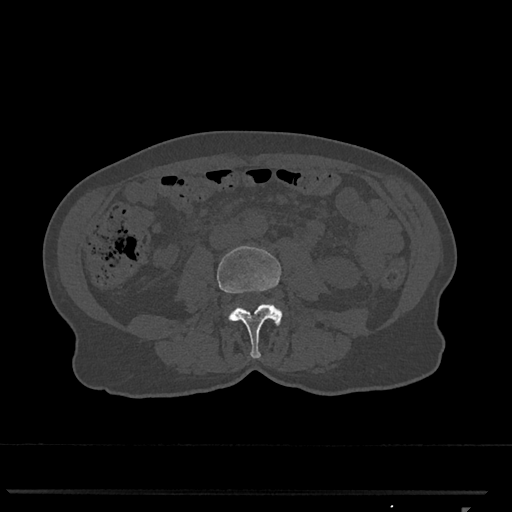
CT including the spine, one axial slice; position 259 of 793 along the scan axis; reconstruction kernel Br40s/3; bone window (W 1800 / L 400 HU); 0.5 mm slice thickness; 512 × 512 image matrix, field of view 380 × 380 mm. Patient: female, 62 years. Case-level facts recorded for this patient, not image findings: primary cancer: renal.
Outlined on this slice (semi-automatic segmentation, software-assisted and operator-edited):
- L3 vertebra: bounding box <217,246,283,358> (left, top, right, bottom; pixels)